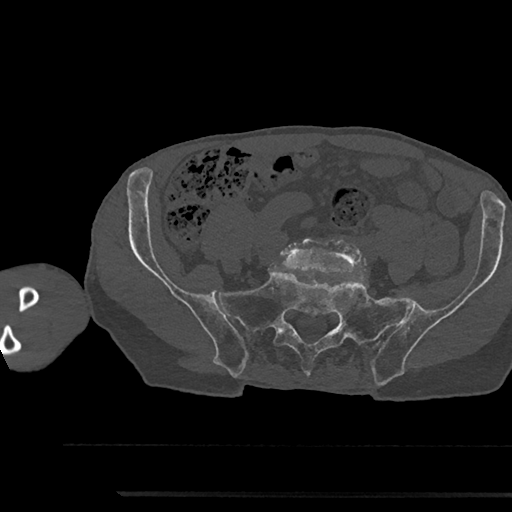
CT including the spine, one axial slice. Slice 299 of 797 in the series (ordered by position). Reconstruction kernel Br40s/3. Bone window (W 1800 / L 400 HU). 0.5 mm slice thickness. 512 × 512 image matrix, field of view 367 × 367 mm. Patient: male, 79 years. Case-level facts recorded for this patient, not image findings: primary cancer: prostate.
Structures marked on this image (semi-automatic segmentation, software-assisted and operator-edited):
- L5 vertebra: box from (x=280, y=237) to (x=367, y=275) px